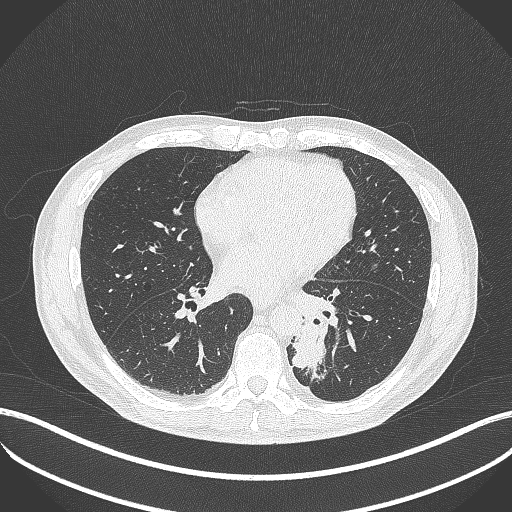
Chest CT, one axial slice. Position 174 of 451 along the scan axis. 120 kVp. Lung window (W 1500 / L -600 HU). 512 × 512 image matrix, field of view 400 × 400 mm. Patient: male, 72 years. From the clinical record (not read from this slice): clinical TNM (as recorded): T2b N0 M1.
Structures marked on this image (rectangle marked by the reading radiologist):
- lung tumour (recorded histology: adenocarcinoma): bounding box <287,311,331,374> (left, top, right, bottom; pixels)